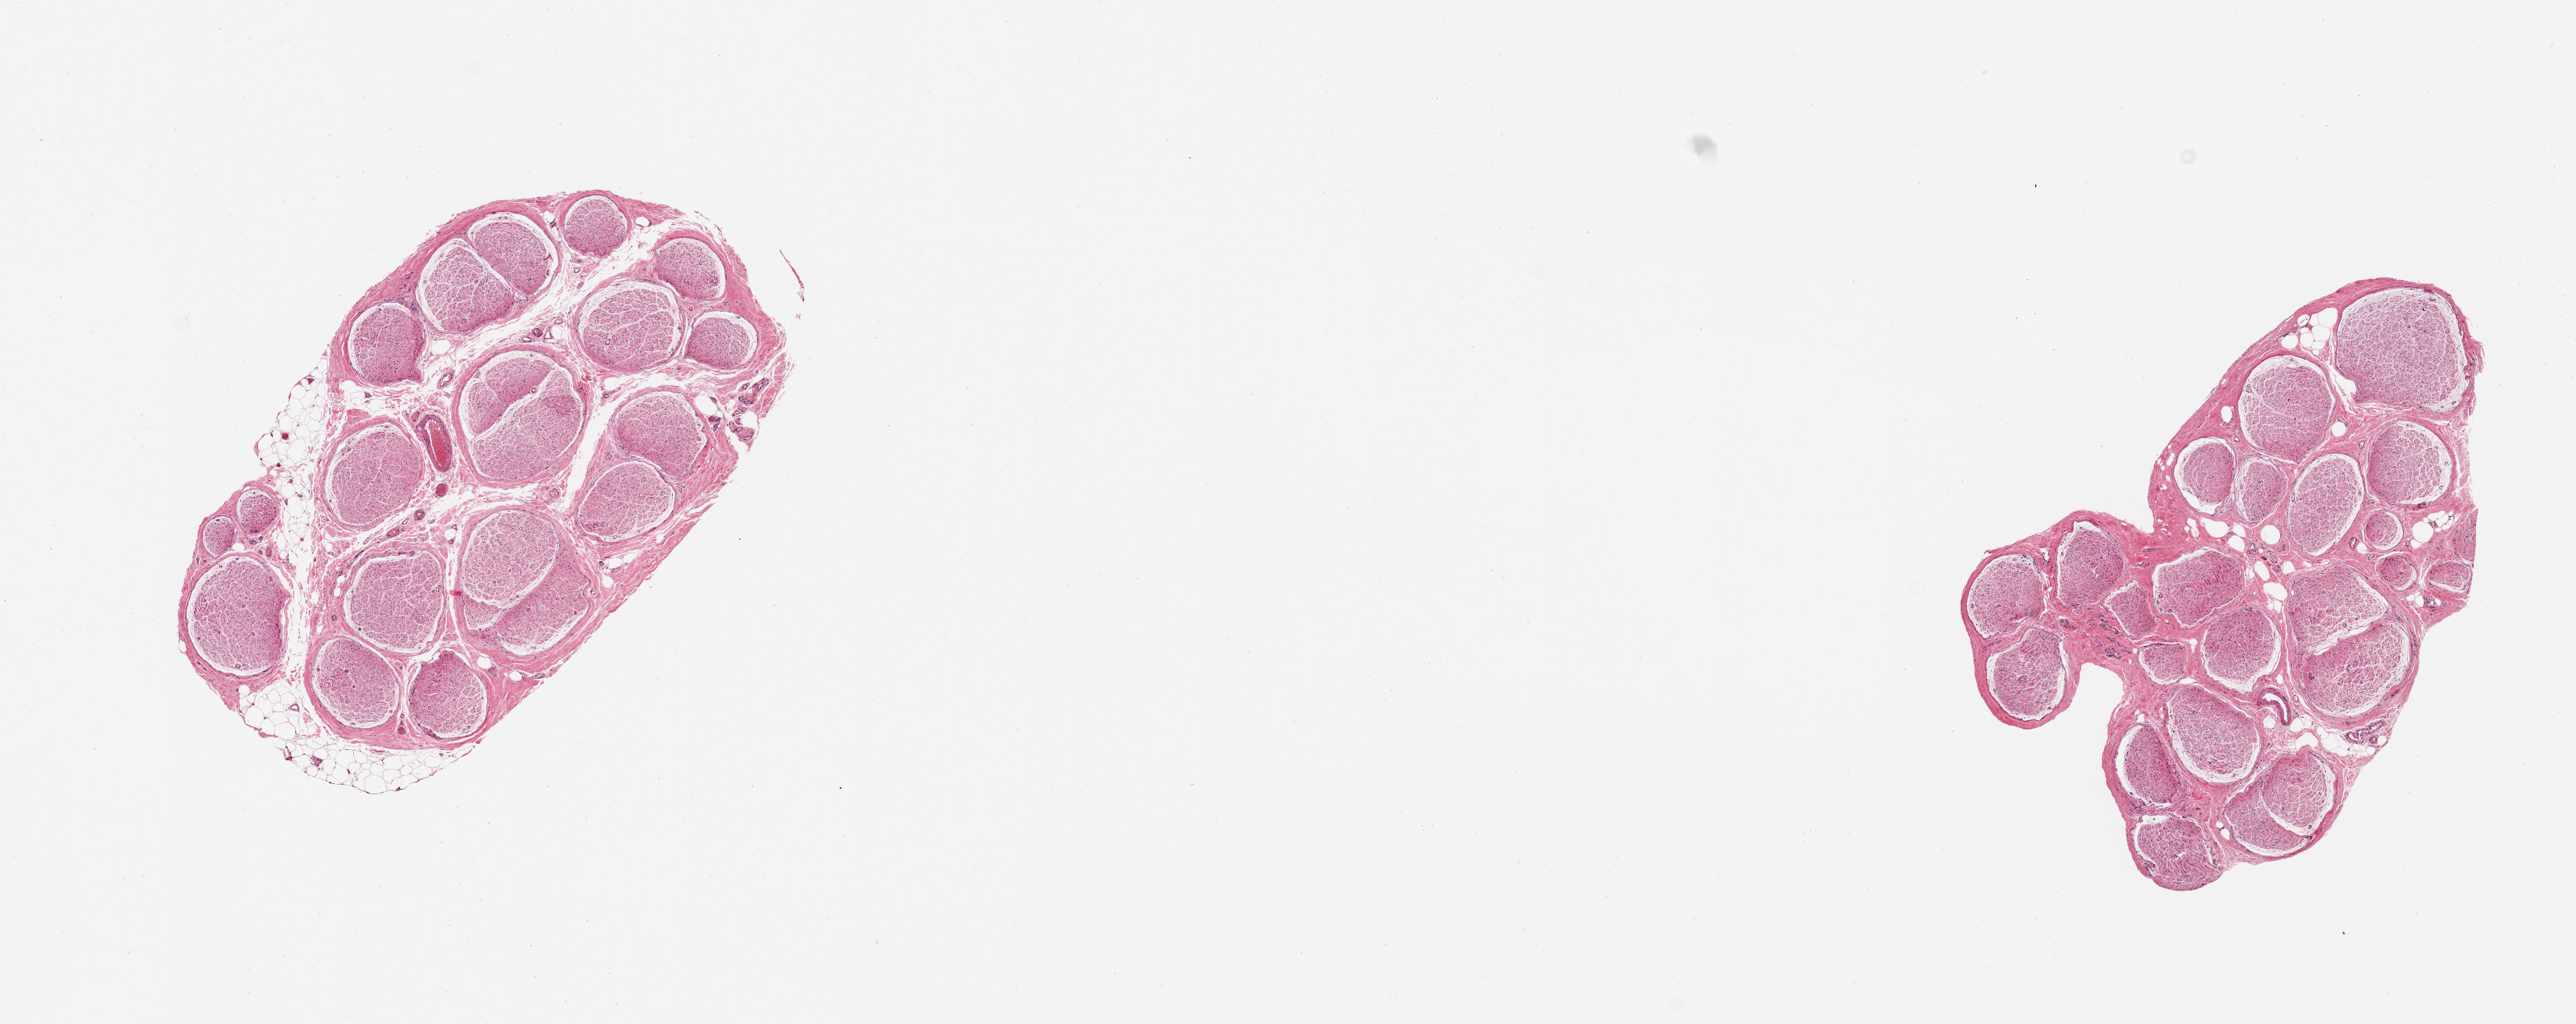
Whole-slide image, haematoxylin and eosin stain, brightfield — shown as a low-resolution overview of the whole scanned area (about 14.8 x 5.9 mm); PAXgene-fixed, paraffin-embedded tissue; target tissue: tibial nerve; donor tissue sample. Donor: female.
• reviewer comment on this tissue sample: 2 pieces; ~10% external/internal fat